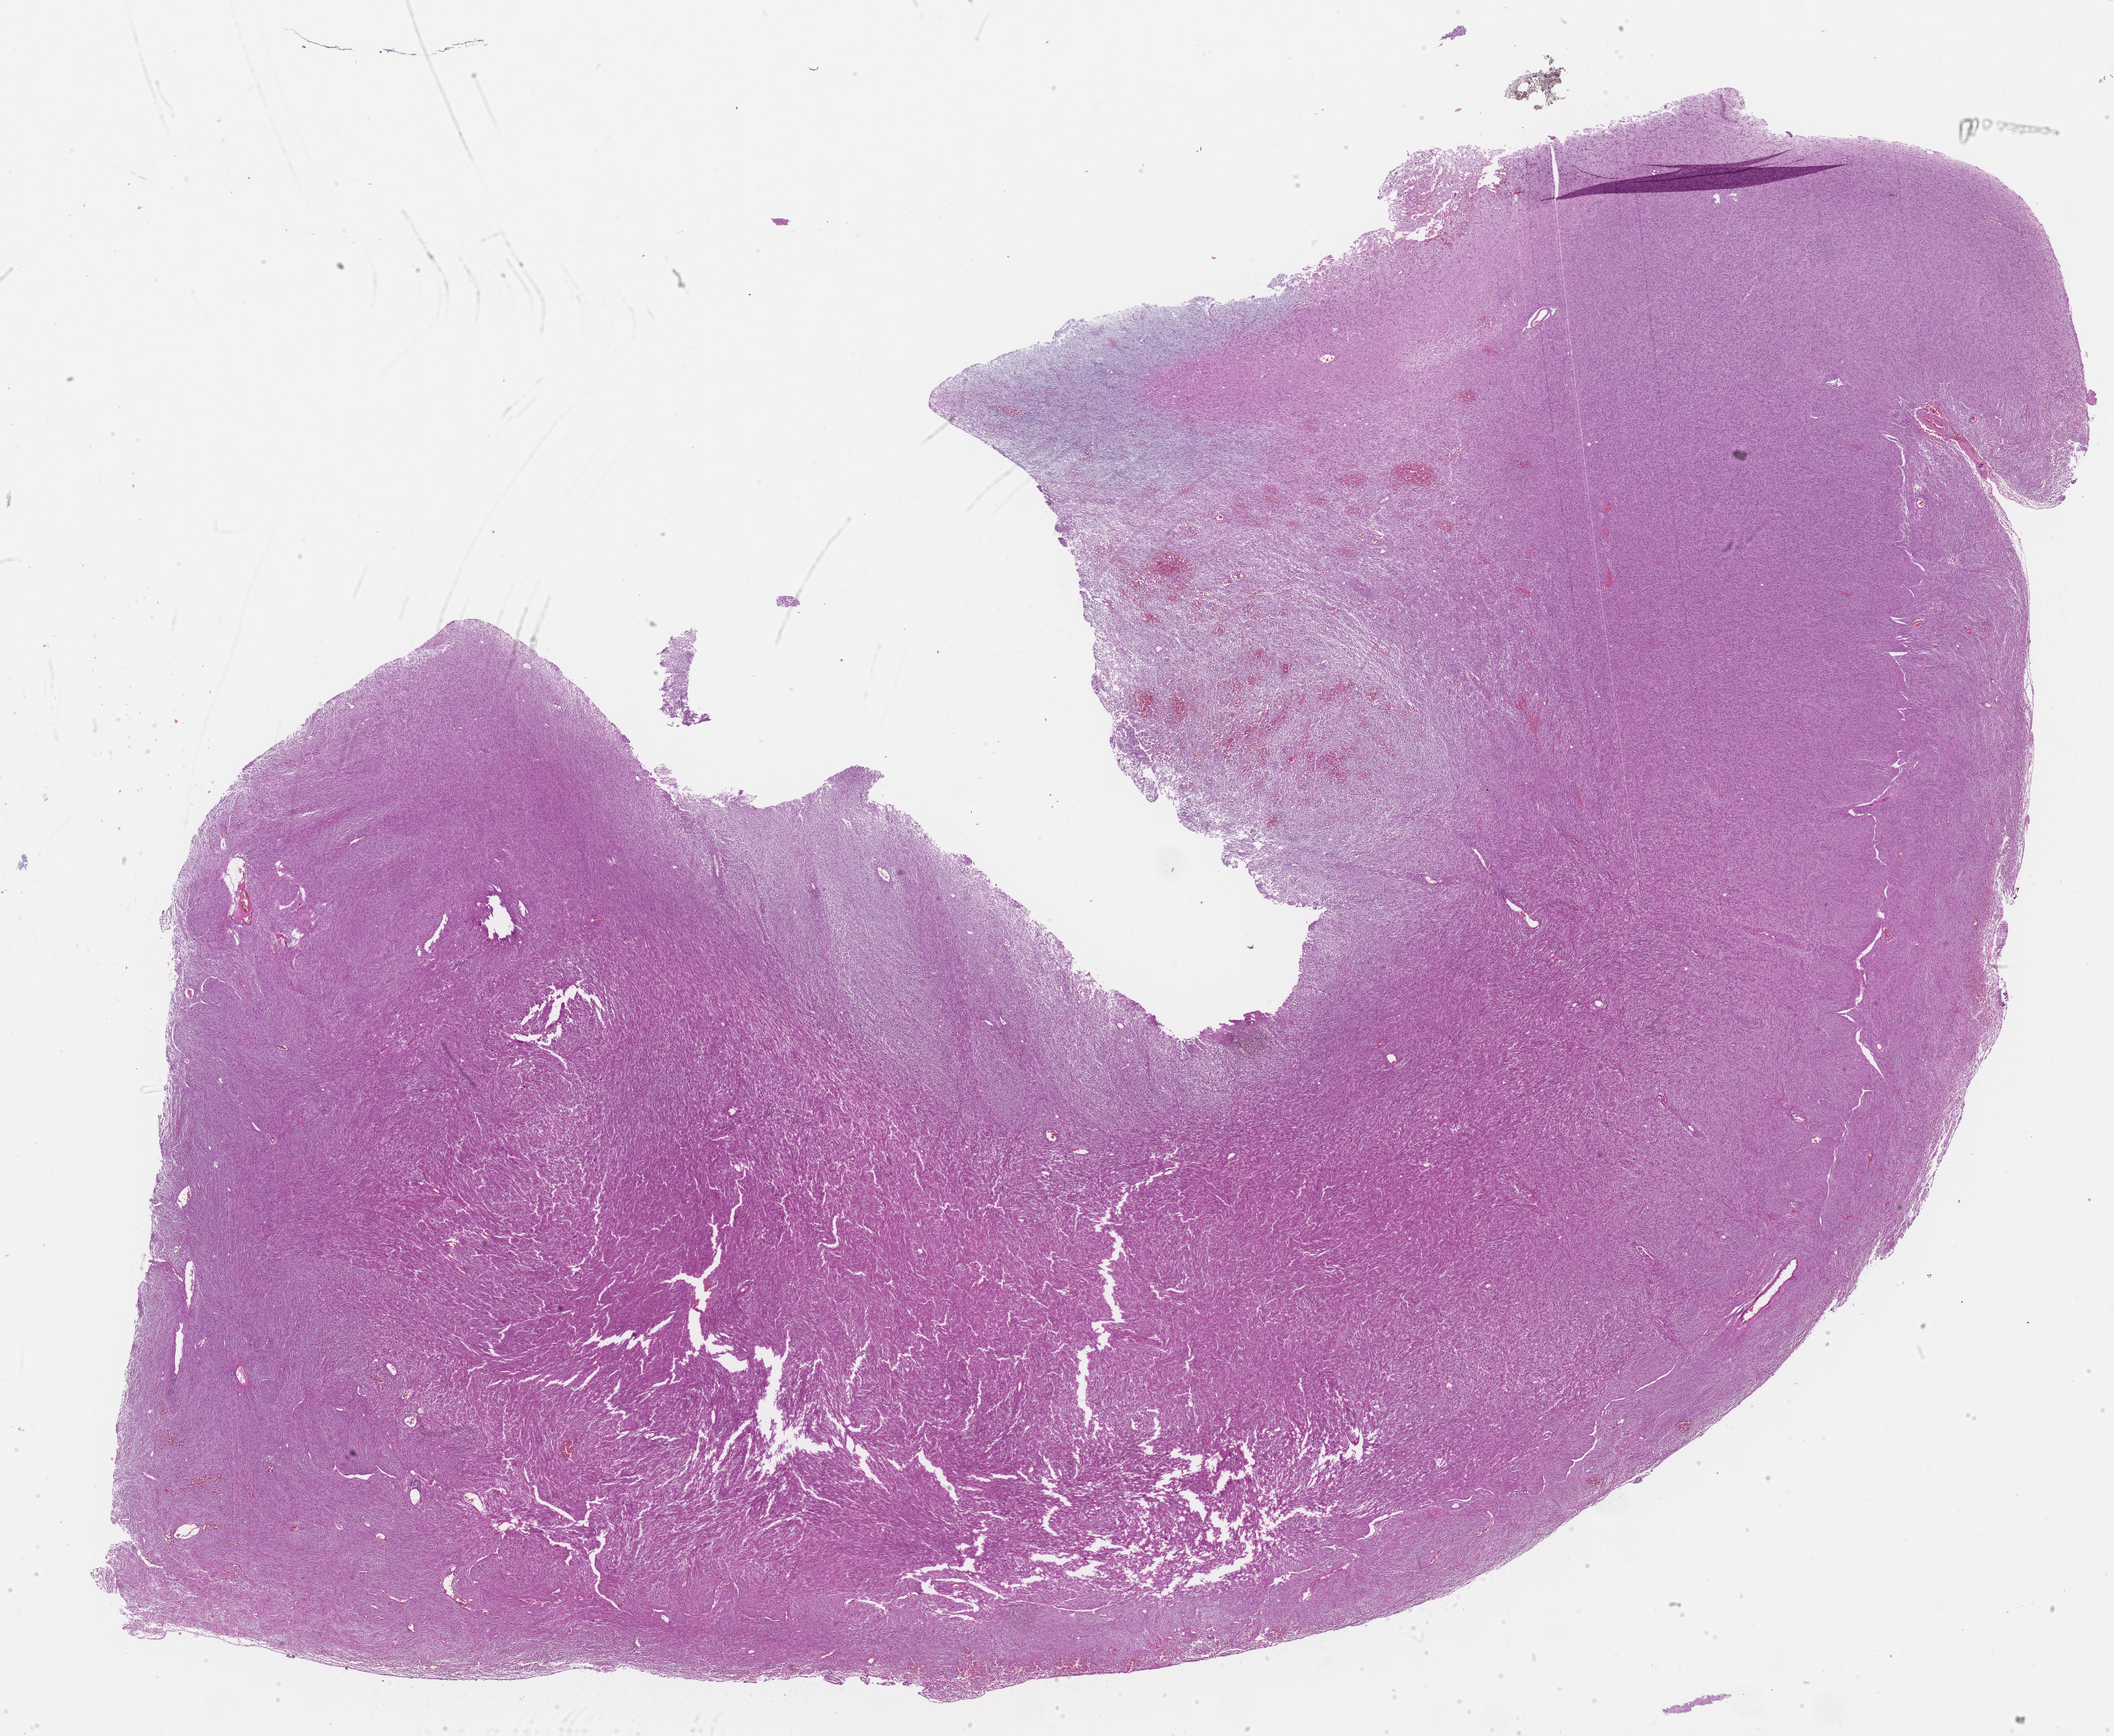
Digitized Hematoxylin and eosin (H&E) stained tissue section (whole slide) — a low-resolution overview of the entire scanned area, about 23.2 x 19.1 mm (slide scanned at 40x). FFPE section. Sample: primary tumour, brain. Patient: female, age at initial diagnosis 62 years.
Histologic diagnosis: Glioblastoma.